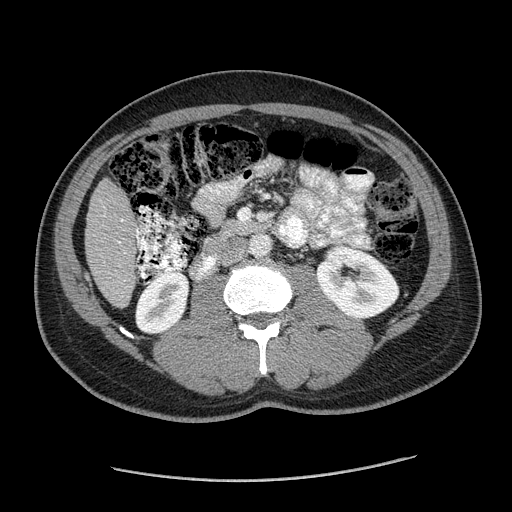
Contrast-enhanced abdominal CT (liver protocol), one axial slice. Position 47 of 182 along the scan axis. Reconstruction kernel STANDARD. Soft-tissue window (W 400 / L 40 HU). 2.5 mm slice thickness. 512 × 512 image matrix, field of view 400 × 400 mm. From the clinical record (not read from this slice): diagnosis: hepatocellular carcinoma (patient treated with transarterial chemoembolisation; whether this scan precedes or follows treatment is not stated here); TNM stage (as recorded): Stage-I; Child-Pugh class: A; tumour differentiation: well differentiated; tumour nodularity: uninodular.
Structures marked on this image (semi-automatically segmented with operator editing):
- liver parenchyma outside the tumour (the mass and vessels are separate outlines, so this box may not span the whole liver): bounding box <84,178,138,306> (left, top, right, bottom; pixels)
- liver vessels: <118,219,124,243>